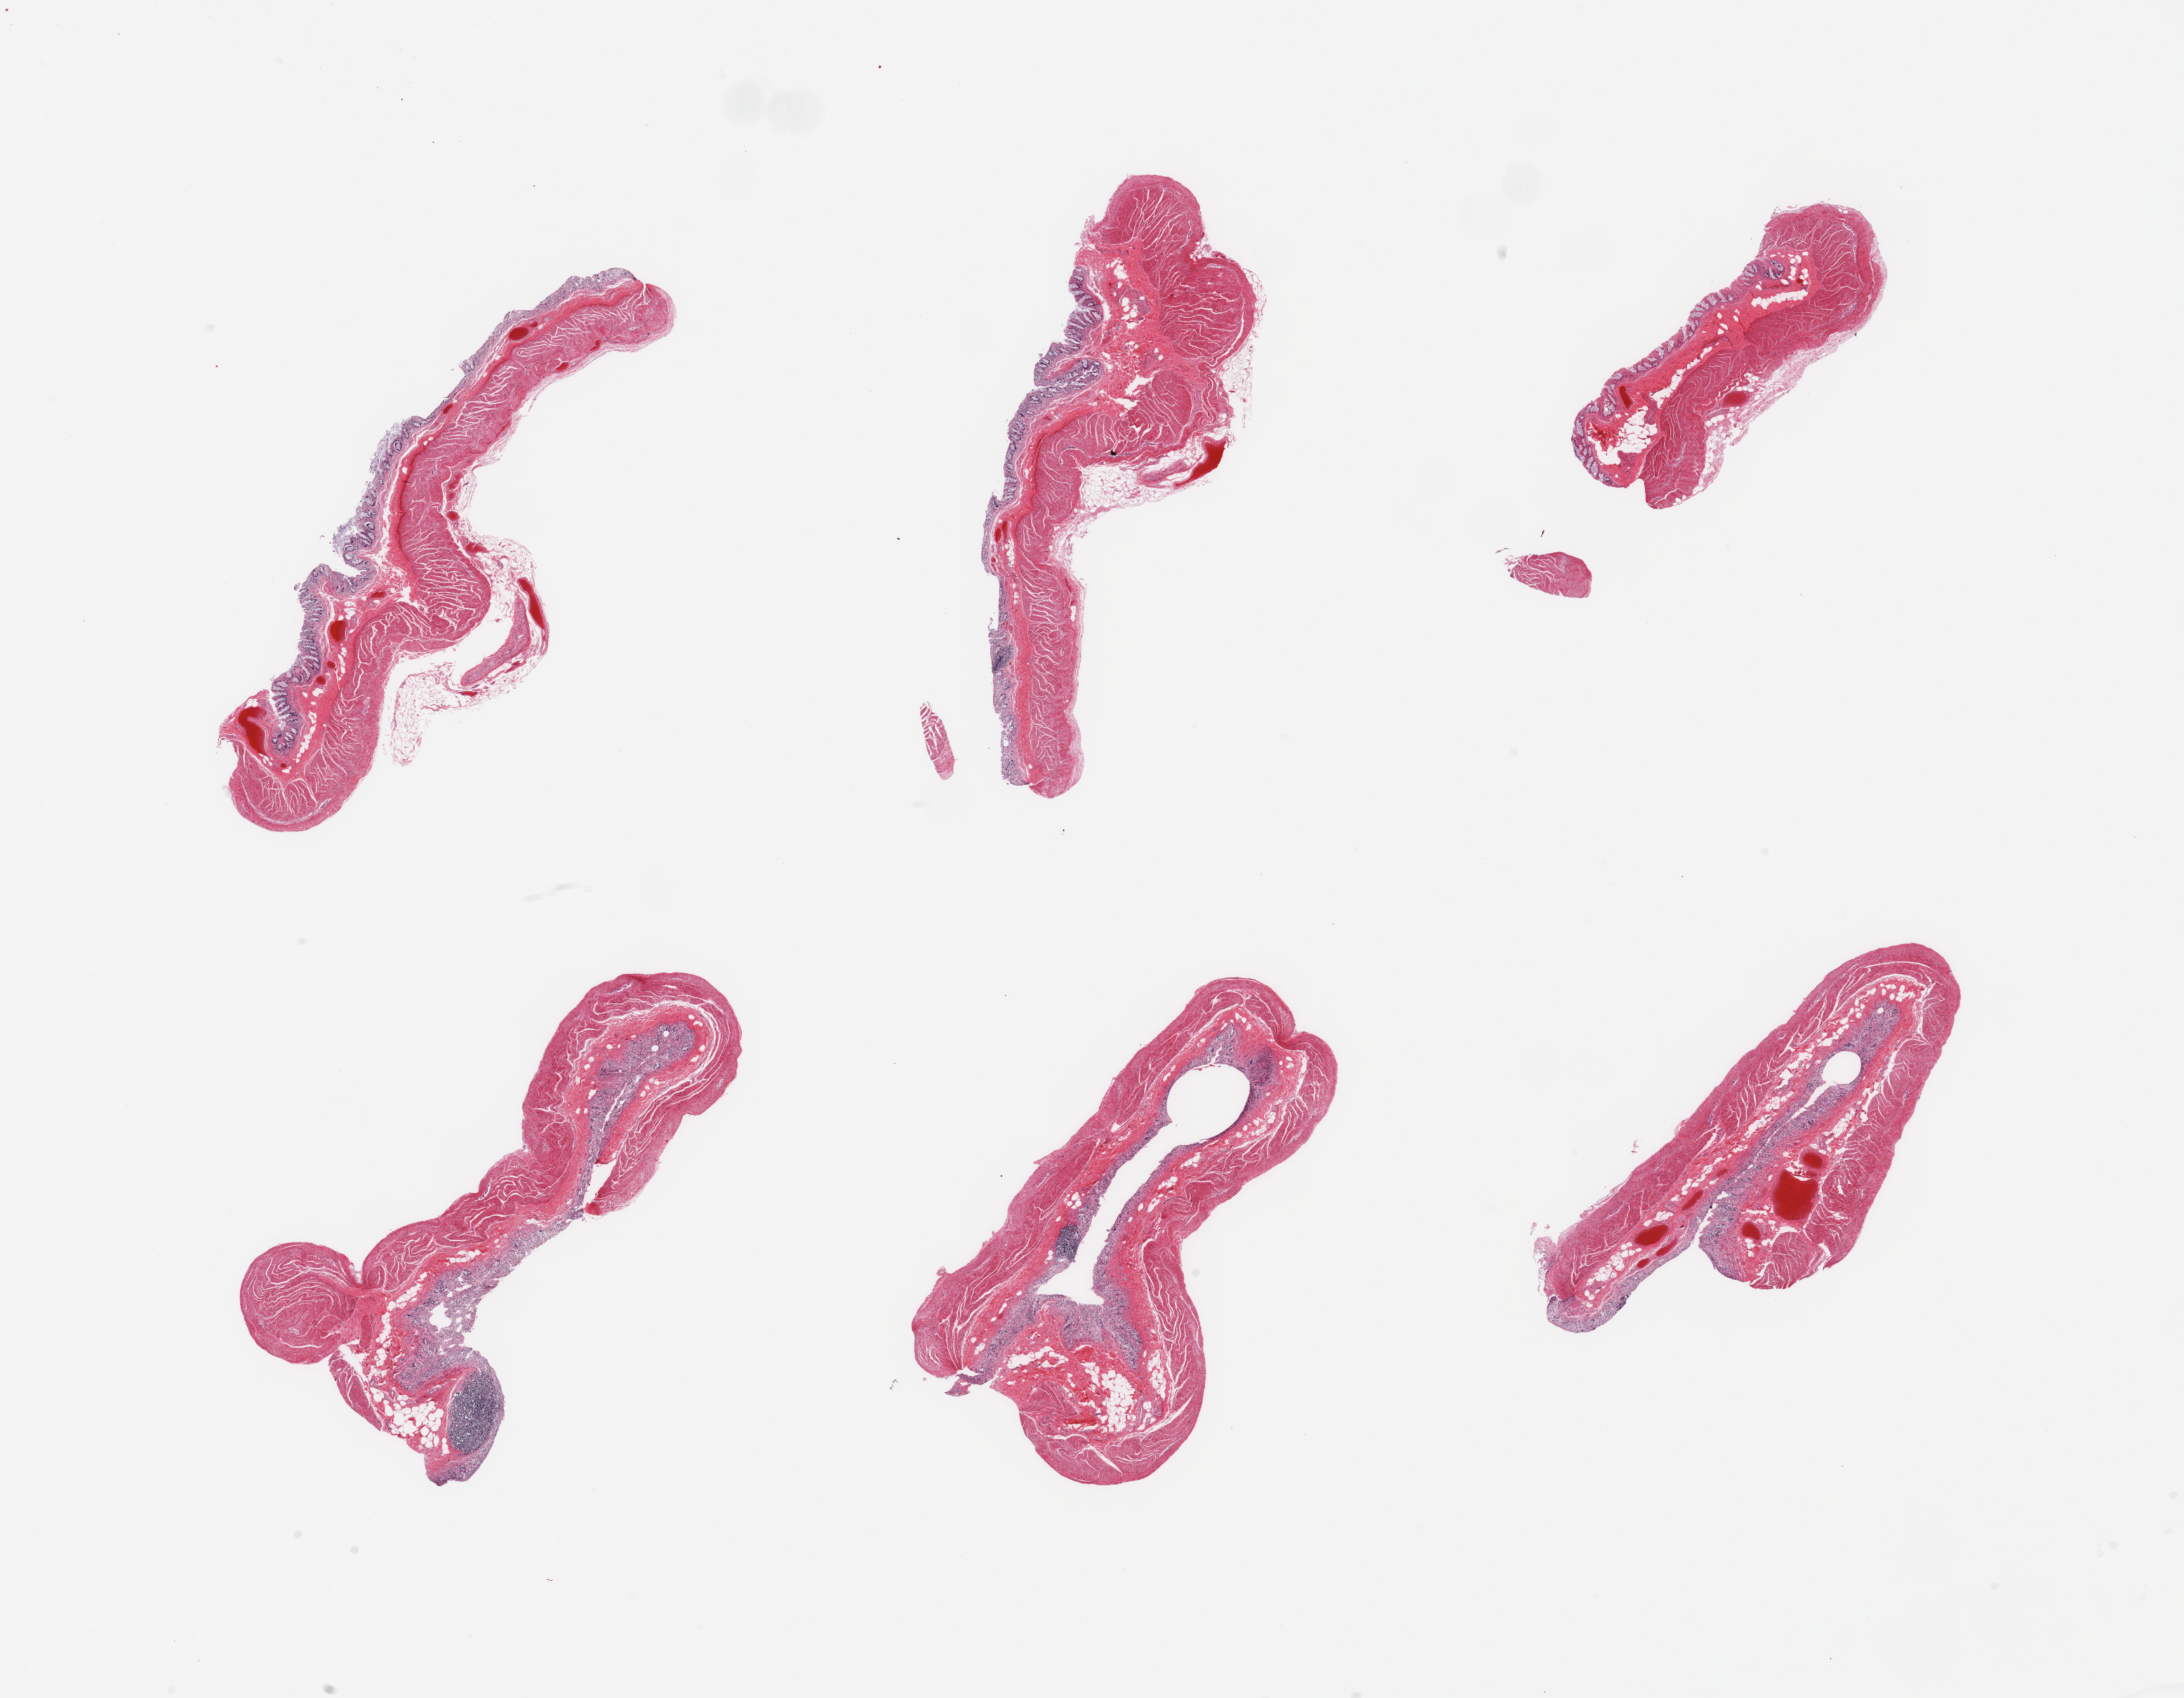
H&E whole-slide image, low-resolution overview of the scanned area, about 24.6 x 19.1 mm. PAXgene-fixed paraffin-embedded (PFPE) section. Section of transverse colon (target tissue). Tissue donor sample.
Reviewer comment on this tissue sample: 6 pieces; mucosa=2-3; muscularis=1-2.